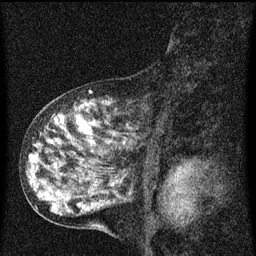
Breast MRI (dynamic contrast-enhanced), one sagittal slice; position 30 of 60 along the scan axis; dynamic contrast-enhanced series, image 2 of 3 at this slice position (ordered by acquisition); 1.5 T; TE 4.2 ms, TR 8 ms; 2 mm slice thickness; 256 × 256 image matrix, field of view 180 × 180 mm. Female patient, age 55 years.
Annotated regions visible in this slice (semi-automatically segmented with operator editing):
- analysis volume of interest (the breast-tissue region the enhancement analysis was run in; not a lesion): bounding box <38,92,151,159> (left, top, right, bottom; pixels)
- tumour enhancement mask (voxels above the 70 % enhancement threshold inside the analysis volume of interest): <56,116,125,145>